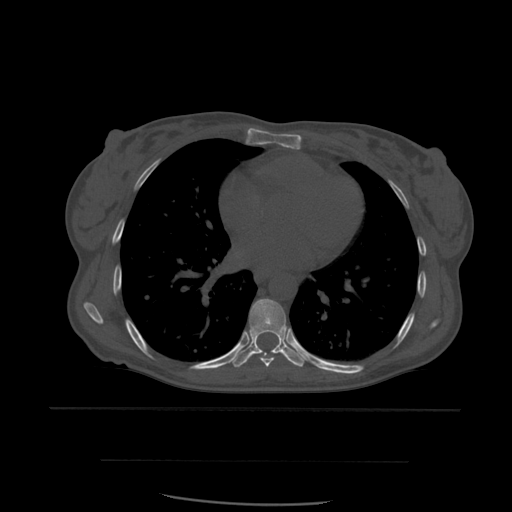
CT including the spine, one axial slice; position 363 of 574 along the scan axis; bone window (W 1800 / L 400 HU); 1.25 mm slice thickness; 512 × 512 image matrix. Patient age 48 years. From the clinical record (not read from this slice): primary cancer: lung; vertebrae with lytic lesions (as recorded): T11.
Annotated regions visible in this slice (semi-automatically segmented with operator editing):
- T6 vertebra: box from (x=249, y=328) to (x=286, y=339) px
- T7 vertebra: (x=260, y=354)–(x=275, y=368)
- T8 vertebra: (x=232, y=299)–(x=305, y=368)